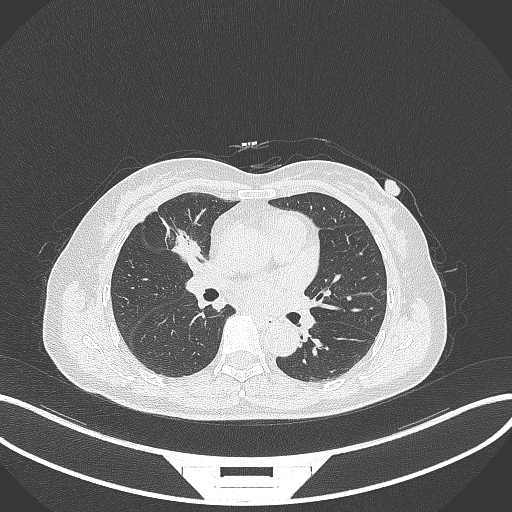
Chest CT, one axial slice. Position 160 of 284 along the scan axis. 120 kVp. Lung window (W 1500 / L -600 HU). 512 × 512 image matrix, field of view 400 × 400 mm. Female patient, age 51 years. From the clinical record (not read from this slice): clinical TNM (as recorded): T1c N0 M0; histopathological grade: G2.
Annotated regions visible in this slice (rectangle marked by the reading radiologist):
- lung tumour (recorded histology: adenocarcinoma): bounding box <168,225,208,268> (left, top, right, bottom; pixels)